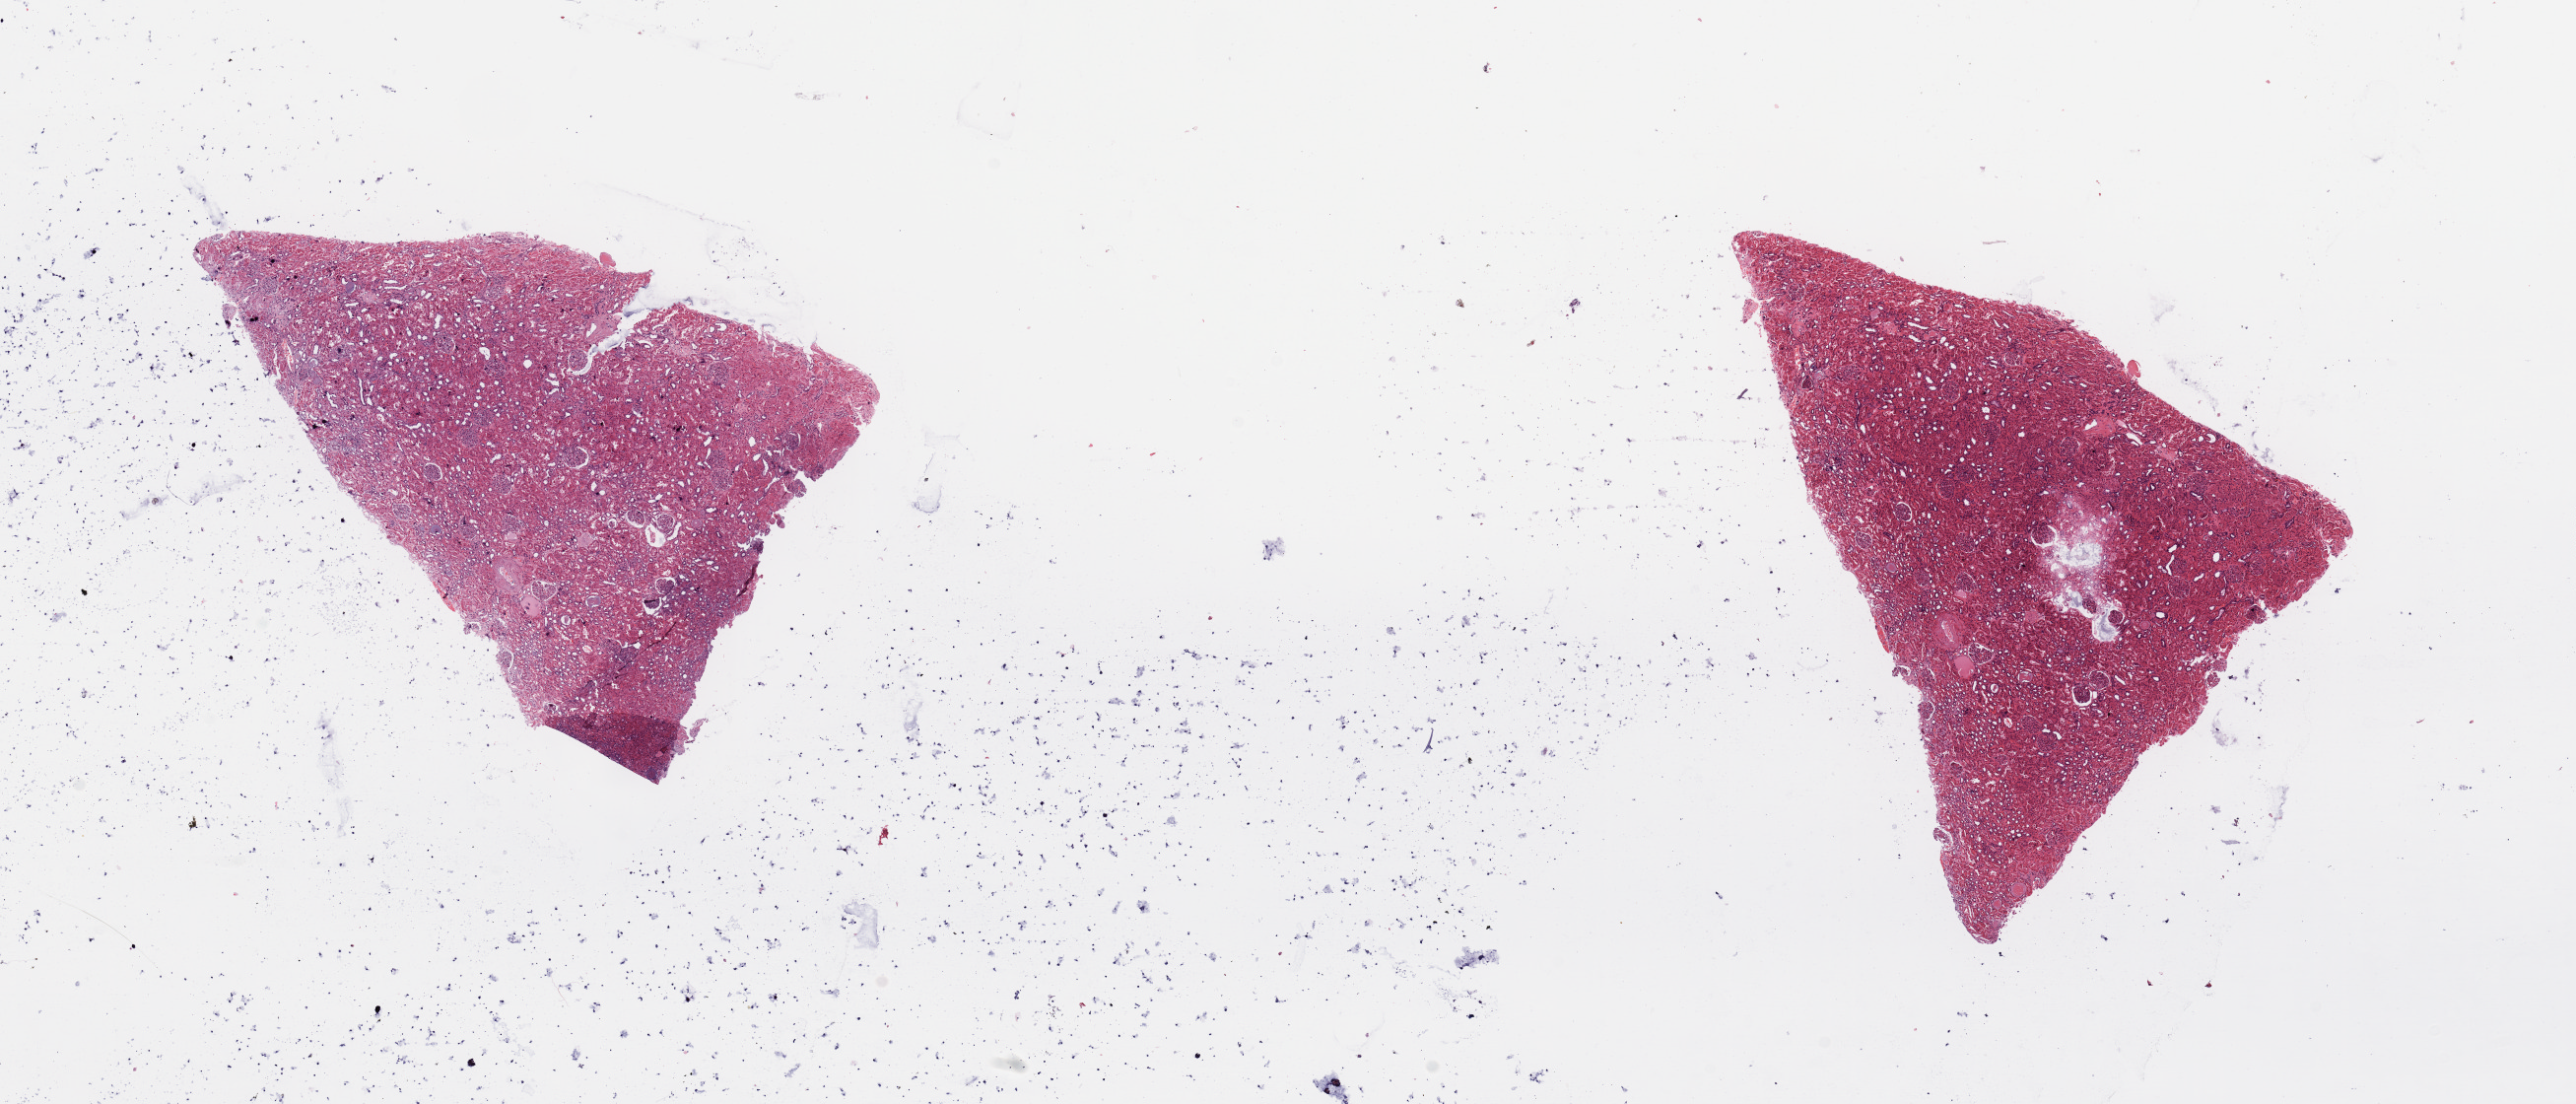
Whole-slide histology image, H&E-stained, whole scanned area (about 20.7 x 8.9 mm, from a 20x scan) shown as a low-resolution overview; normal (non-tumour) tissue sample, sampled site: kidney. Female, 66 y/o.
This section: normal (non-tumour) tissue from the same patient. Patient diagnosis: Renal cell carcinoma, NOS.